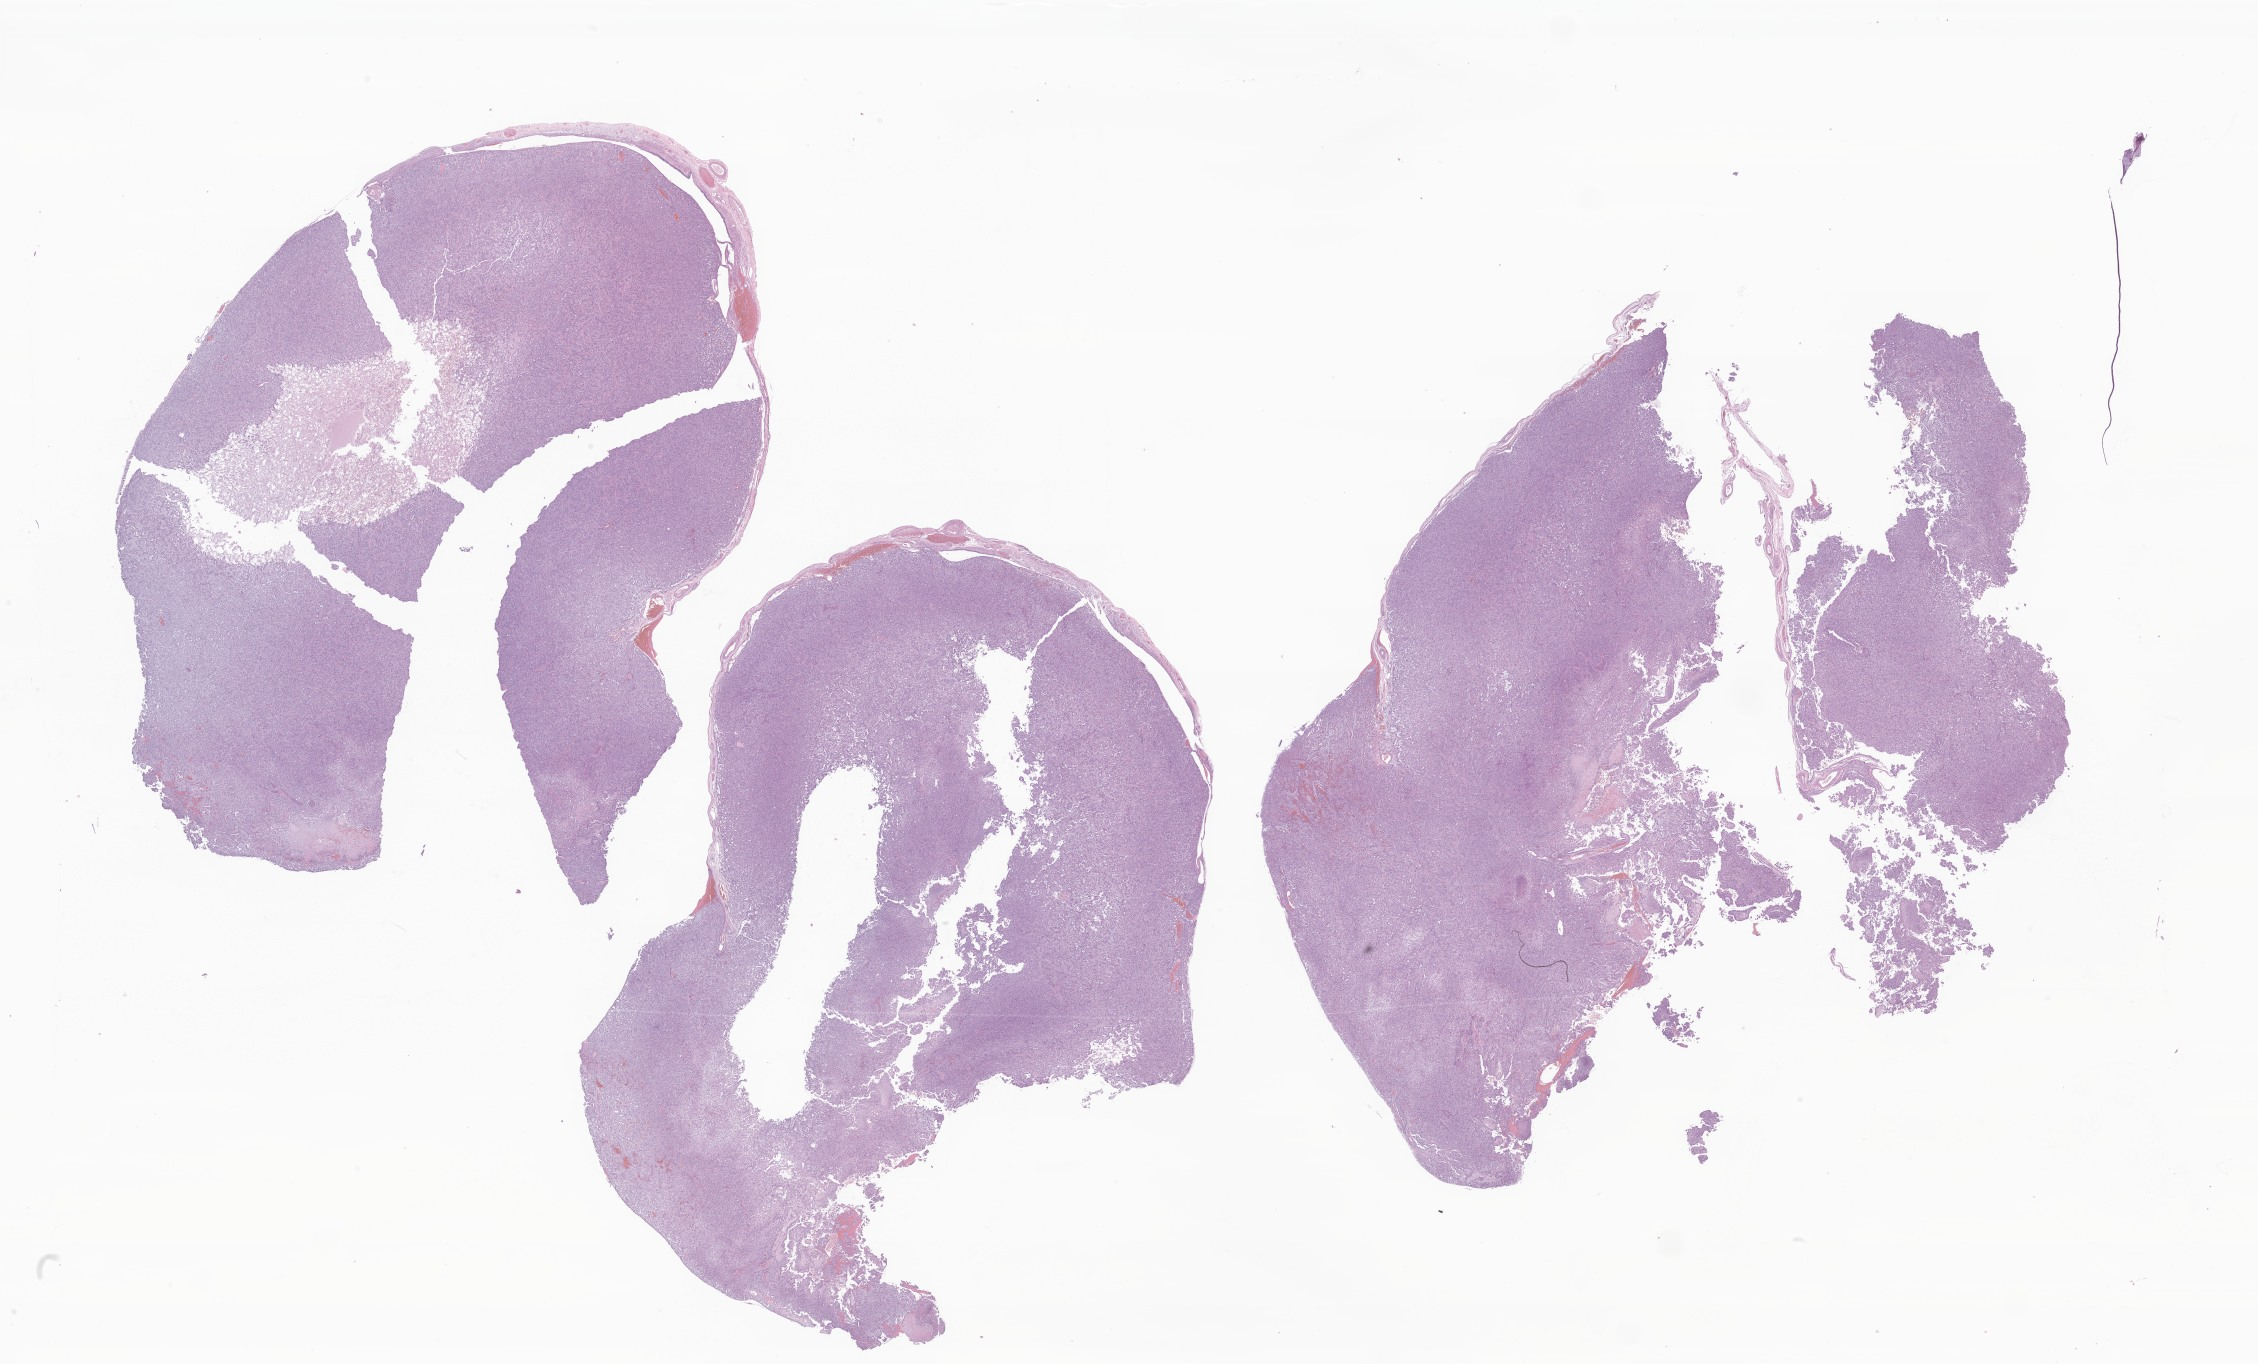
H&E whole-slide image of tumor tissue from the spinal cord — whole scanned area (about 38.1 x 23.0 mm) shown as a low-resolution overview. FFPE section. Patient: male, age 82 months (6 years 10 months).
Diagnosis (ICD-O-3 morphology term): Myxopapillary ependymoma.